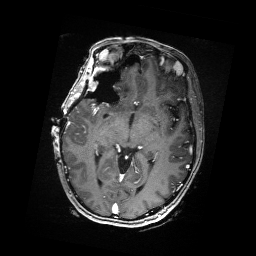
Brain MRI from a brain-tumour surgery series, one axial slice; position 99 of 176 along the scan axis; T1-weighted post-contrast; 1 mm slice thickness; 256 × 256 image matrix. Case-level facts recorded for this patient, not image findings: histopathology: Metastatic Carcinoma from Breast primary.
Annotated regions visible in this slice (manually delineated by an expert):
- residual tumour: bounding box (x1, y1, x2, y2) in pixels: (88, 69, 117, 88)